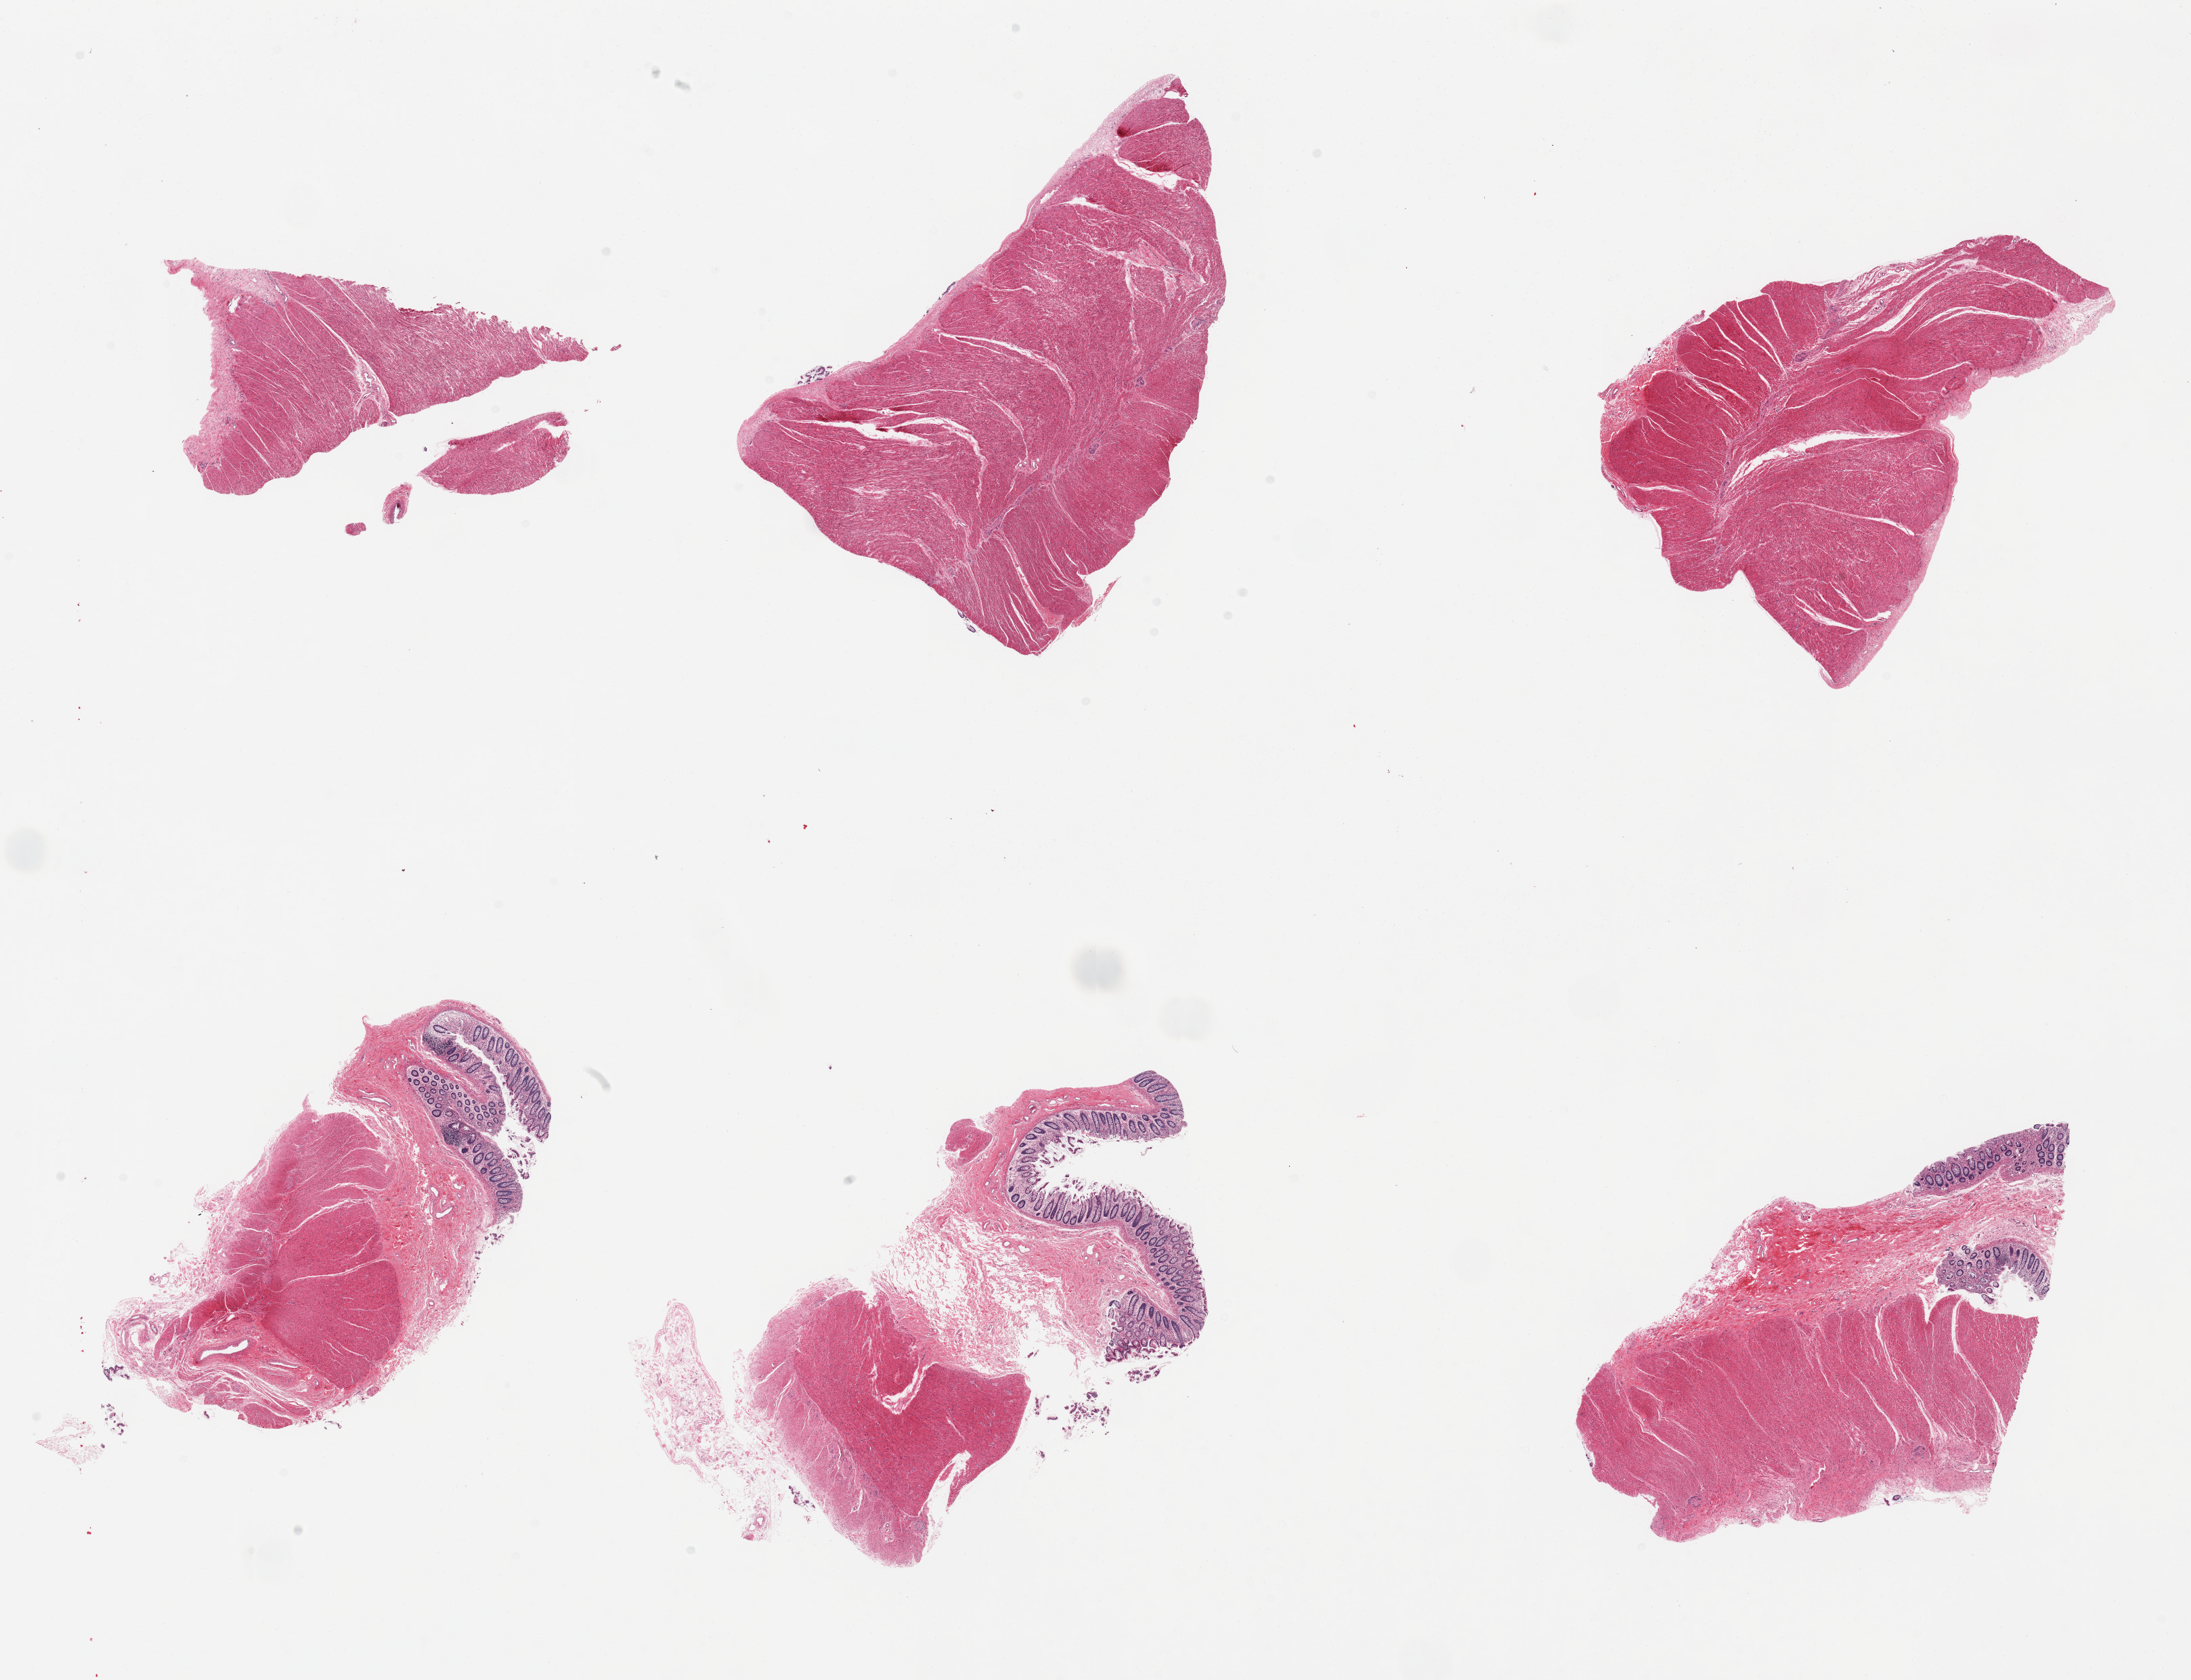
Hematoxylin and eosin (H&E) whole-slide image — shown as a low-resolution overview of the whole scanned area (about 25.6 x 19.6 mm). PAXgene-fixed, paraffin-embedded tissue. Sampled site (target tissue): sigmoid colon. Tissue donor sample. Female donor.
Review note (as recorded): 6 pieces, mainly muscularis, ~10% 'contaminant mucosa' present.